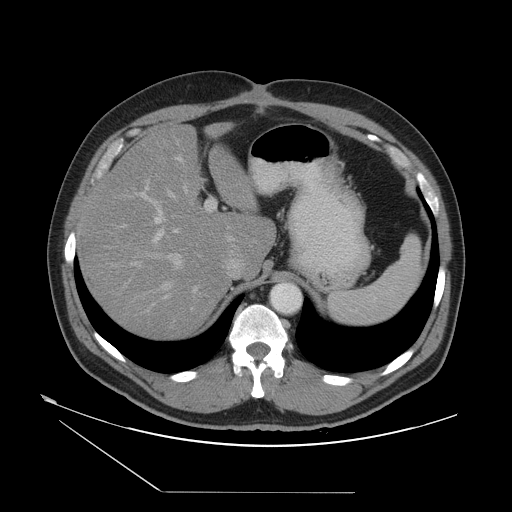
Contrast-enhanced abdominal CT, one axial slice. Position 36 of 55 along the scan axis. Reconstruction kernel STANDARD. 120 kVp. Intravenous contrast given. Soft-tissue window (W 400 / L 40 HU). 5 mm slice thickness. 512 × 512 image matrix, field of view 454 × 454 mm. Male patient, age 59 years. From the clinical record (not read from this slice): diagnosis: colorectal cancer liver metastases, imaged before liver resection; multiple liver metastases: yes; largest metastasis: 0.3 cm; disease in both lobes: yes.
Structures marked on this image (expert manual segmentation):
- hepatic veins: bounding box [x1, y1, x2, y2] px = [144, 181, 198, 295]
- liver: [81, 123, 274, 335]
- planned liver remnant (the part of the liver to remain after resection): [82, 146, 273, 335]
- portal vein (with intrahepatic branches): [122, 156, 234, 310]
- liver metastasis: [125, 162, 132, 171]